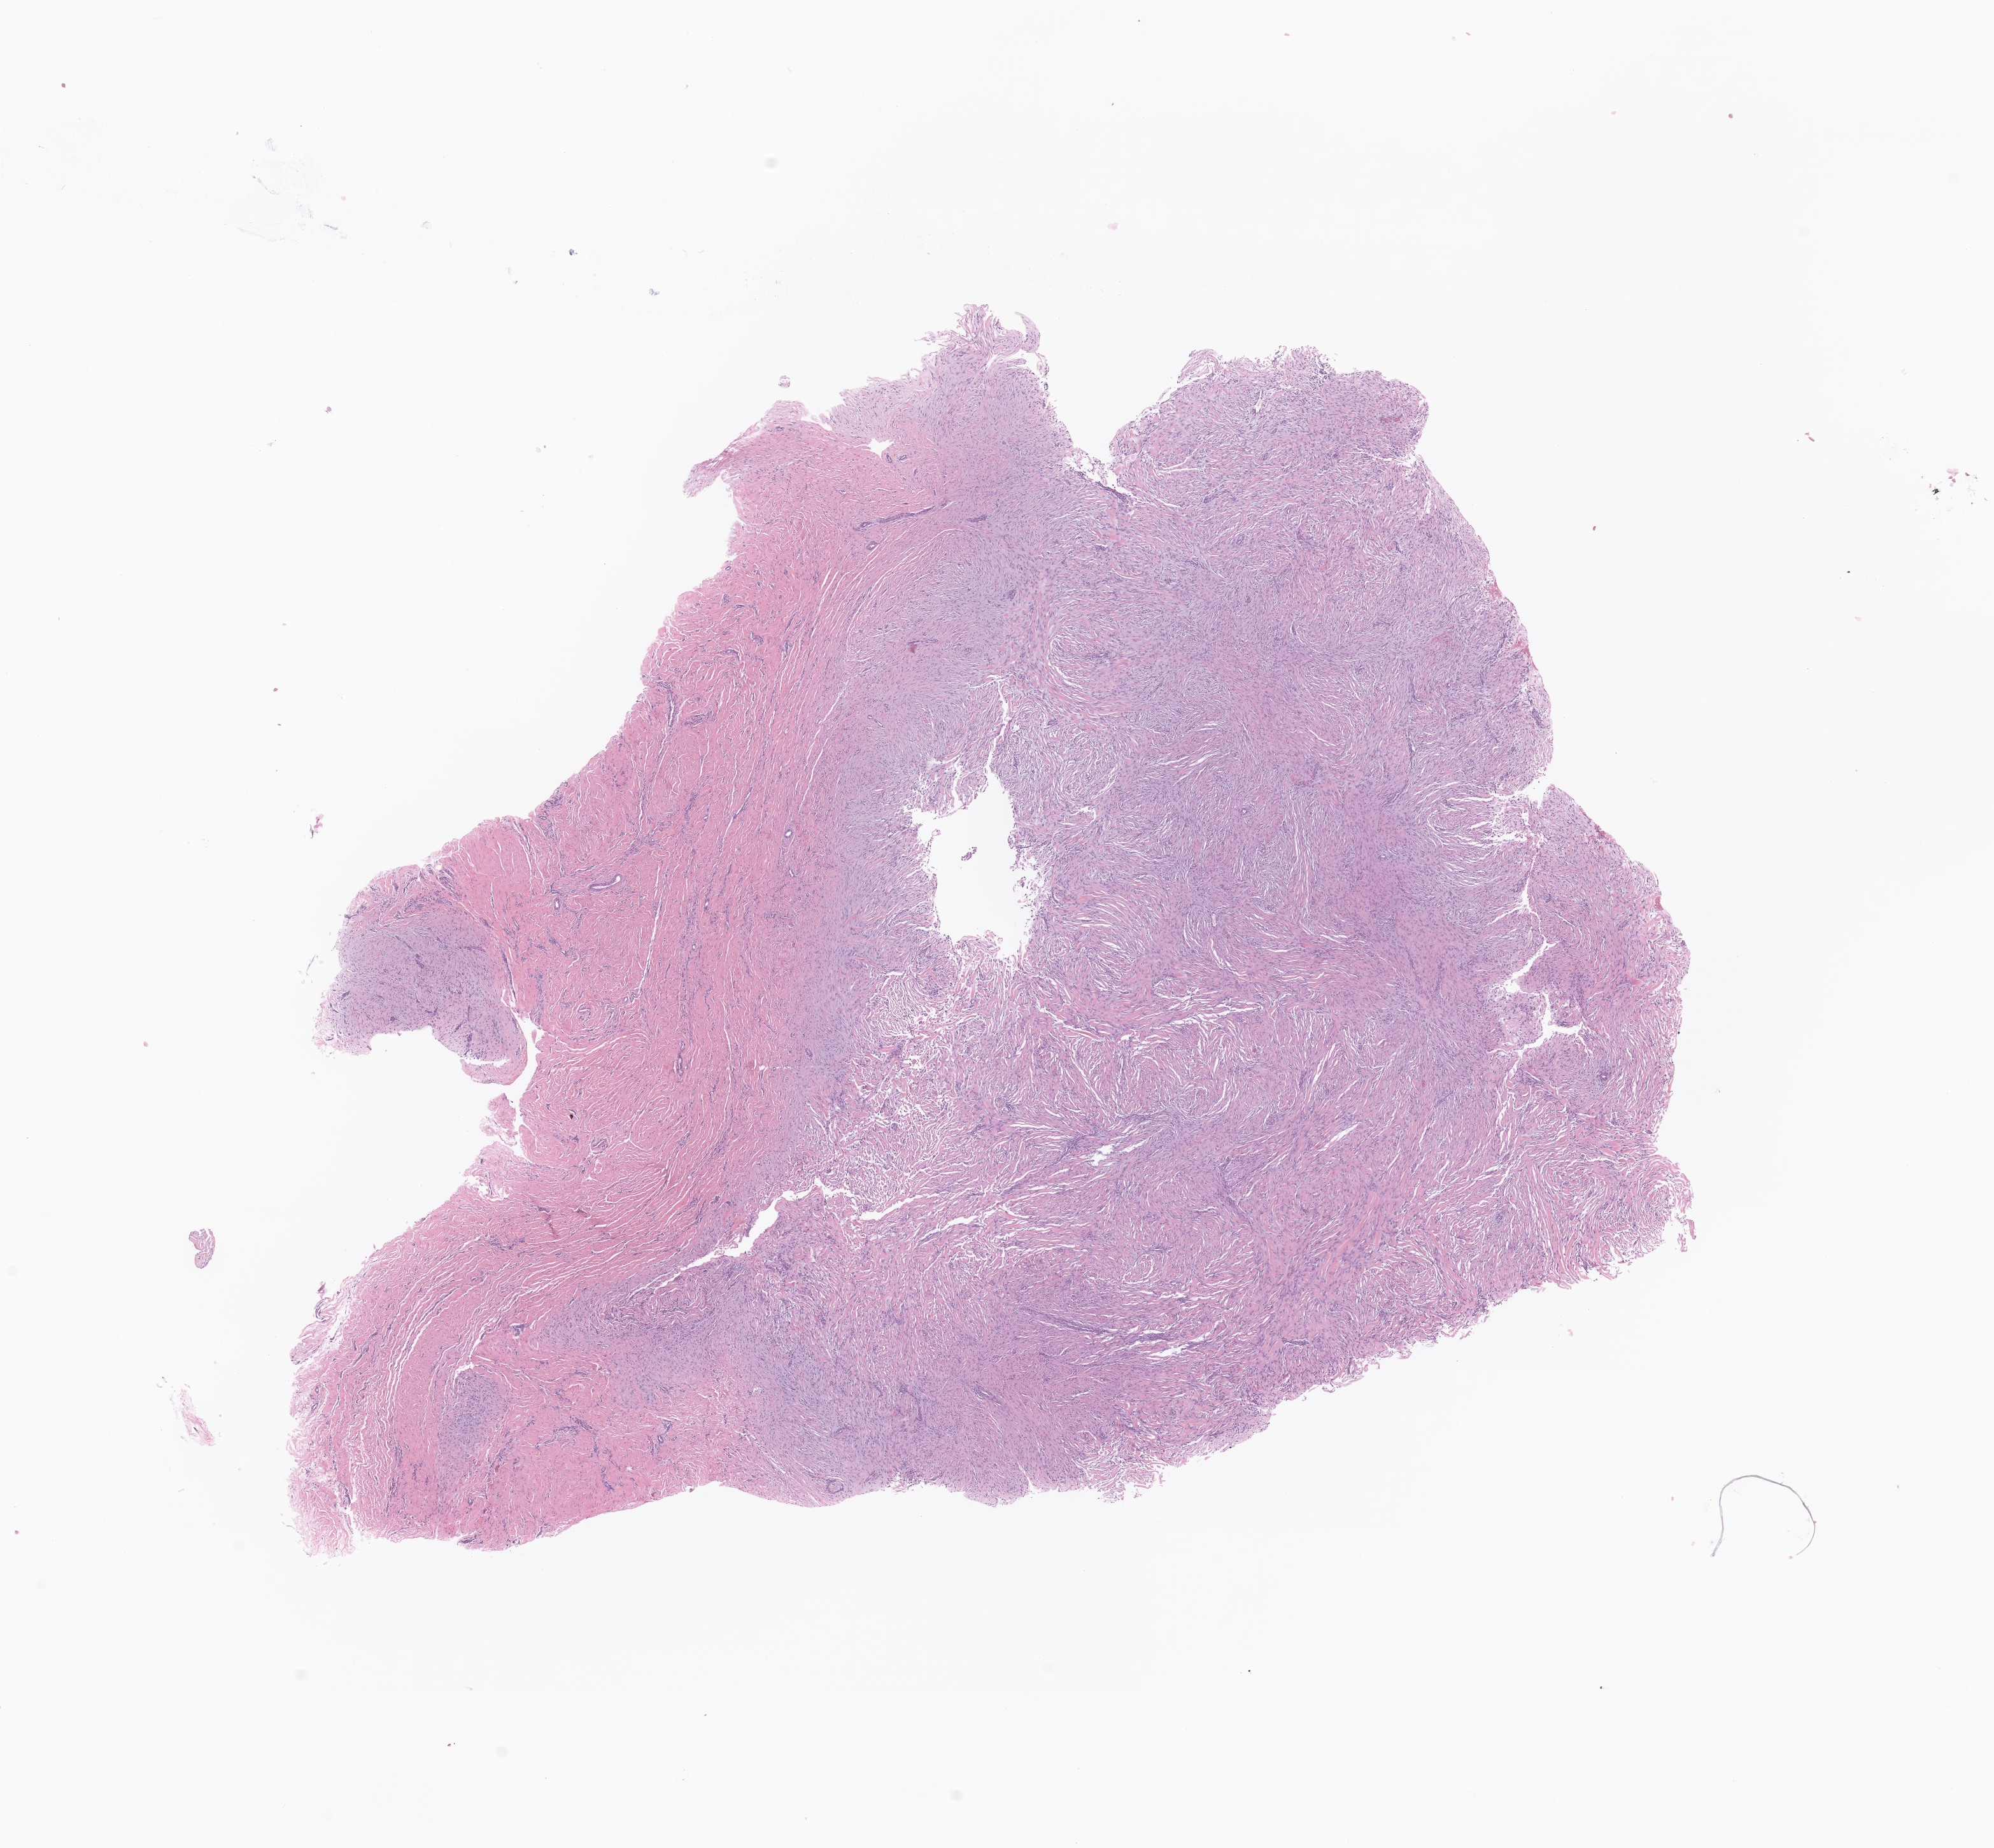
Whole-slide image, haematoxylin and eosin stain of tumor tissue from the soft tissue of upper extremity — a low-resolution overview of the entire scanned area, about 13.2 x 12.2 mm, FFPE section. Patient female; age 942 days (about 2.6 years).
* diagnosis (ICD-O-3 morphology term): Aggressive fibromatosis